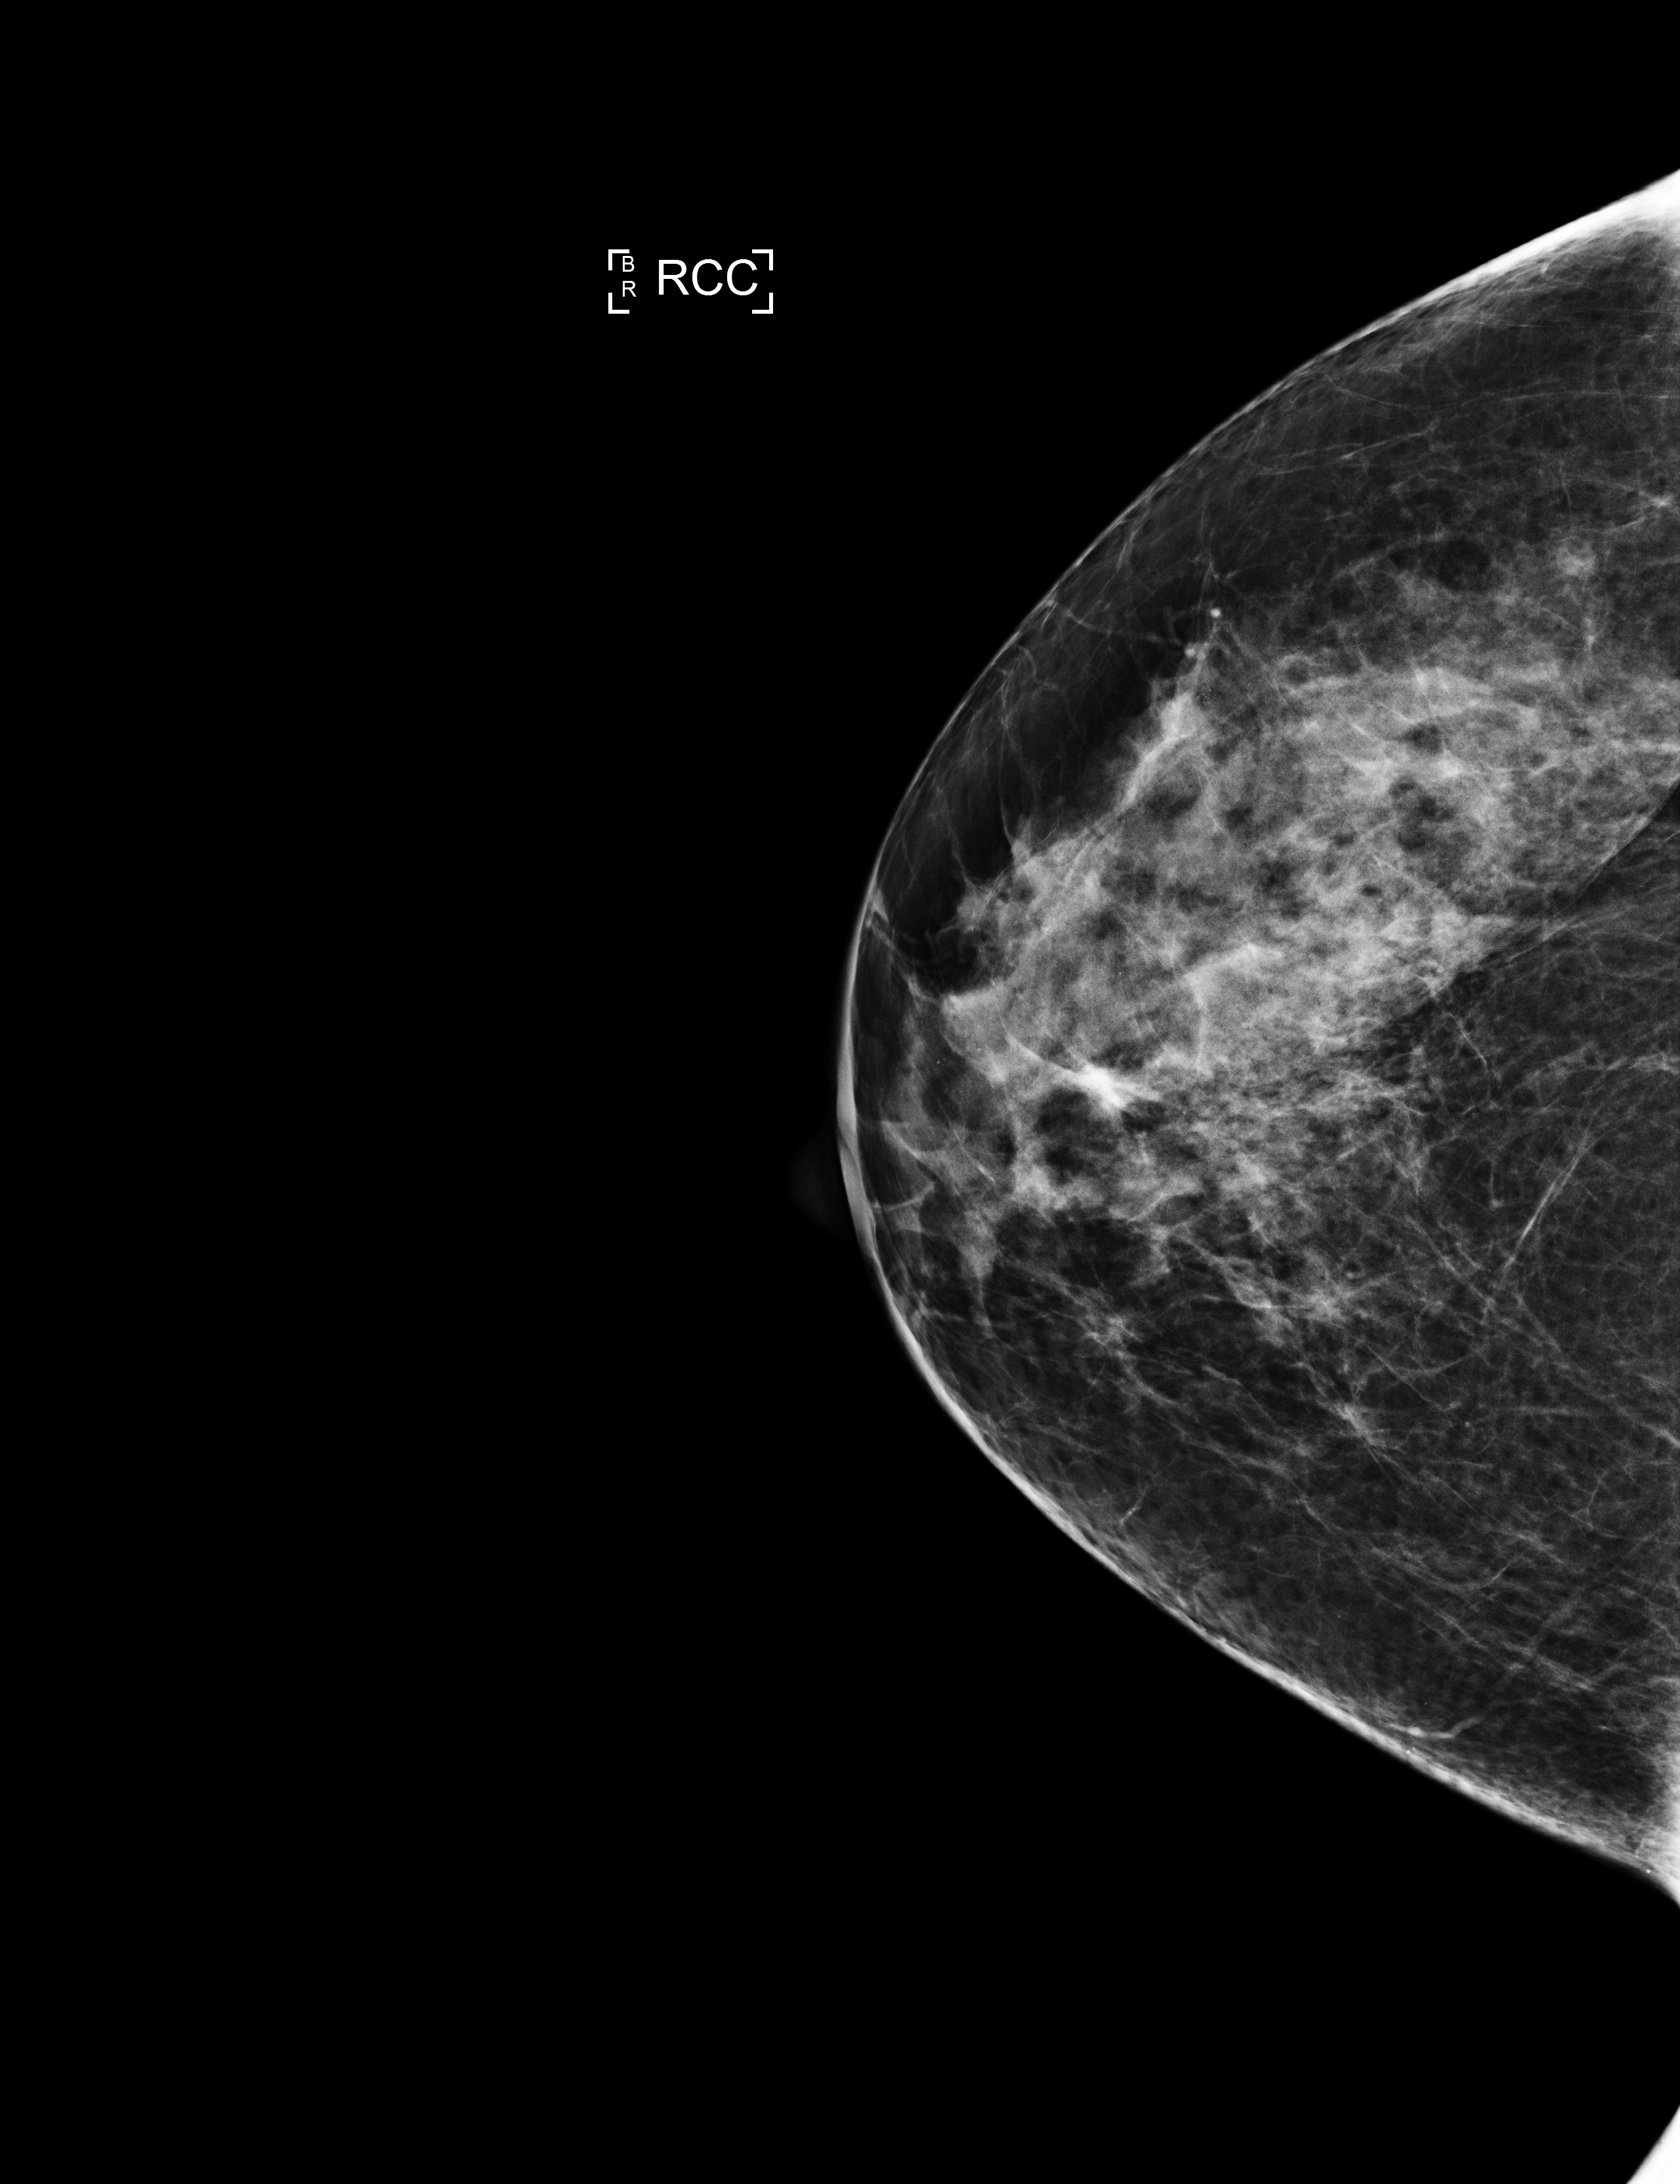
Annual screening mammography examination; compressed breast thickness 61 mm. Female patient, age 56 years.
Image type: full-field digital mammogram. Breast: right. Projection: cranio-caudal projection.